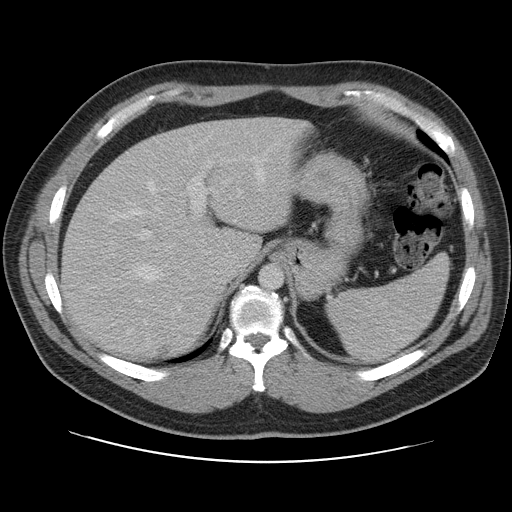
Contrast-enhanced abdominal CT, one axial slice; slice 81 of 109 in the series (ordered by position); intravenous contrast given; soft-tissue window (W 400 / L 40 HU); 5 mm slice thickness; 512 × 512 image matrix, field of view 402 × 402 mm. Male patient, age 35 years. Case-level facts recorded for this patient, not image findings: diagnosis: colorectal cancer liver metastases, imaged before liver resection; multiple liver metastases: yes; largest metastasis: 2.8 cm.
Annotated regions visible in this slice (expert manual segmentation):
- hepatic veins: bounding box [x1, y1, x2, y2] px = [116, 156, 266, 324]
- liver: [62, 118, 302, 359]
- planned liver remnant (the part of the liver to remain after resection): [63, 118, 294, 356]
- portal vein (with intrahepatic branches): [106, 160, 220, 303]
- liver metastasis: [160, 348, 170, 354]